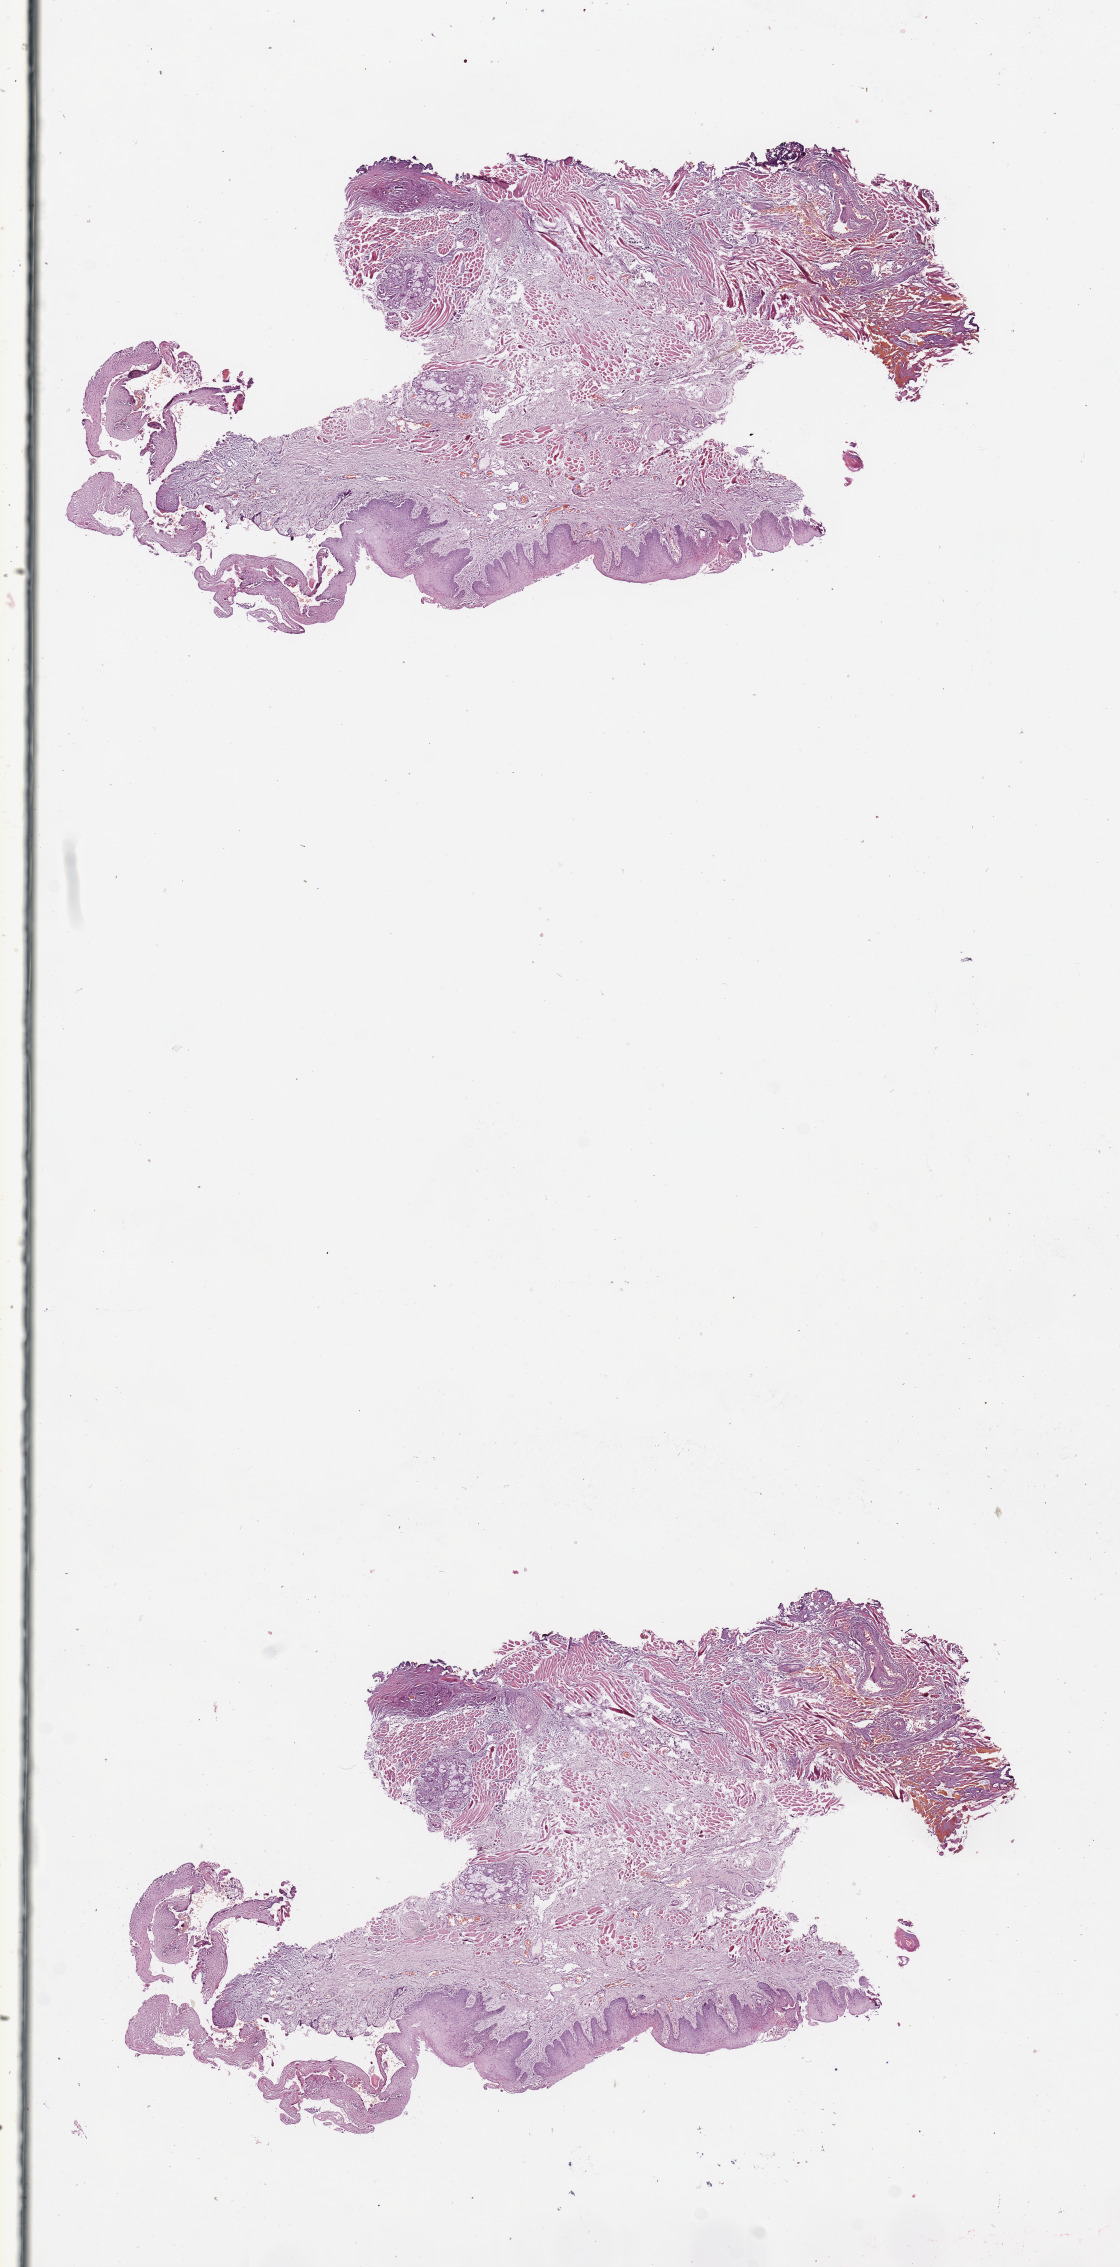
Digitized H&E-stained tissue section (whole slide) — shown as a low-resolution overview of the whole scanned area (about 8.9 x 17.9 mm), head and neck, tissue type not recorded. 58-year-old male patient.
• patient diagnosis: Squamous cell carcinoma, NOS (floor of mouth, NOS)